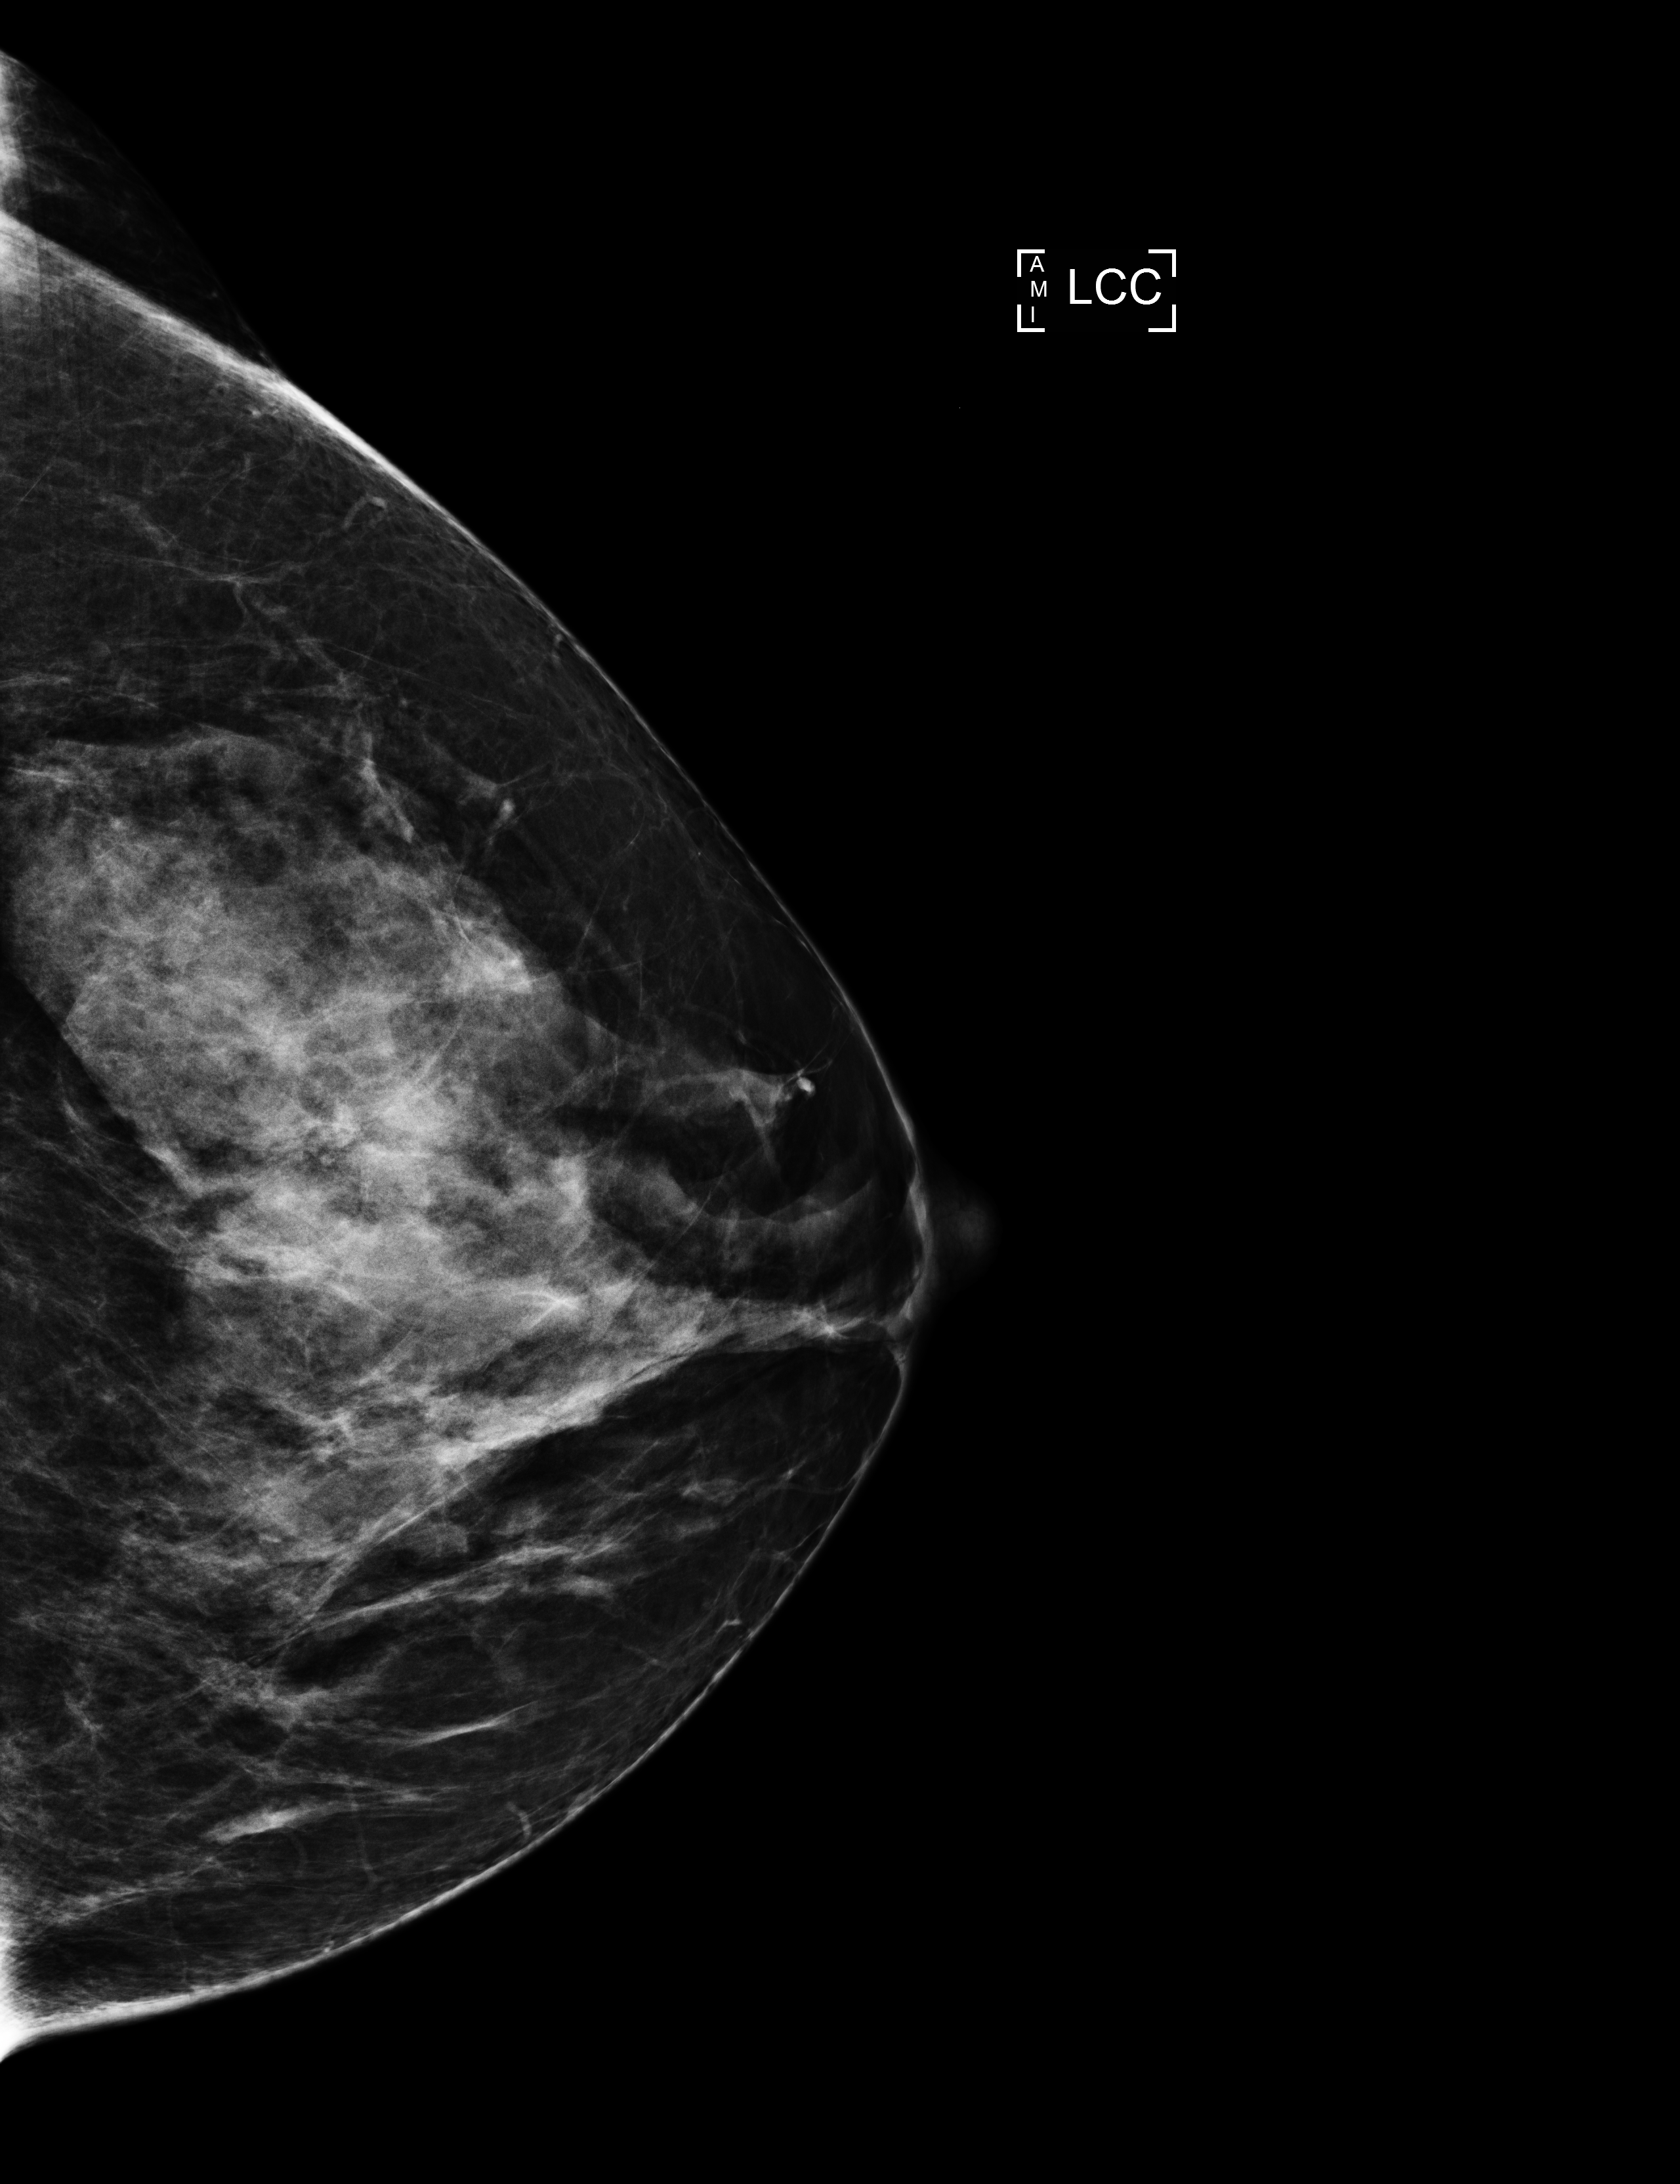
Screening examination, compressed breast thickness 74 mm, system: Selenia Dimensions.
Image type: full-field digital mammogram. Breast: left. Projection: CC view.